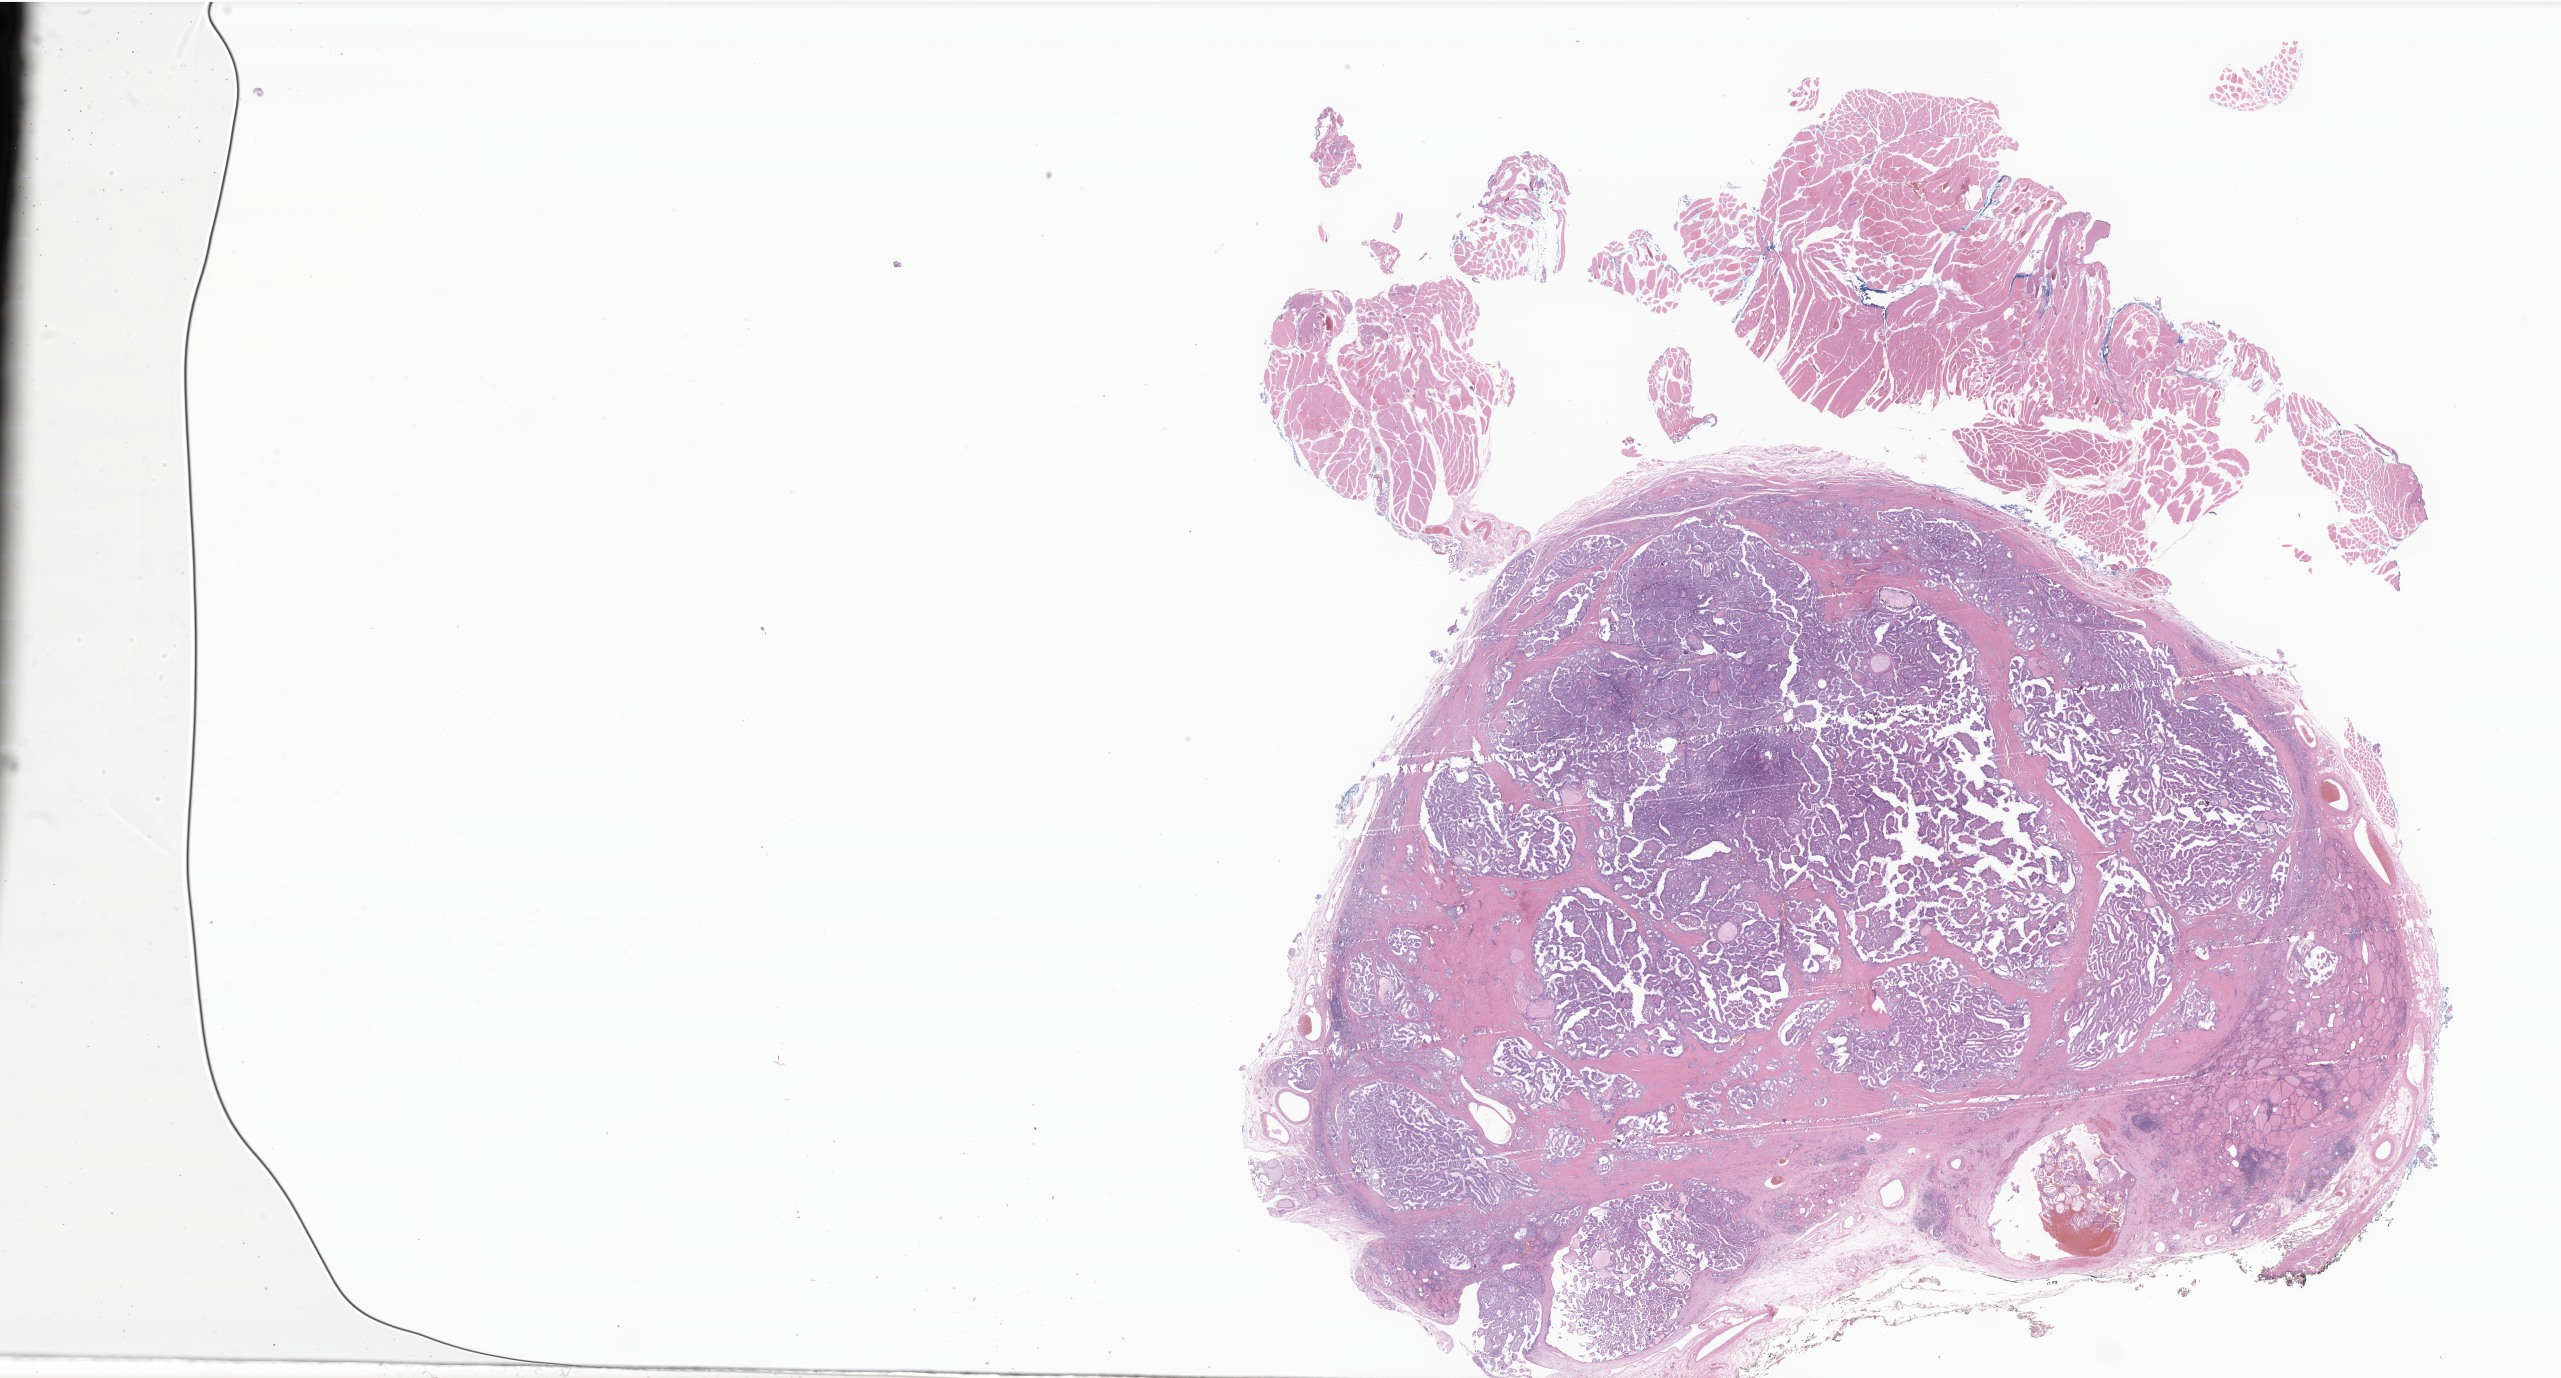
Haematoxylin and eosin whole-slide image of tumor tissue from the thyroid, shown as a low-resolution overview of the whole scanned area (about 43.2 x 23.2 mm), formalin-fixed paraffin-embedded section. Female patient, age 222 months (18 years 6 months).
Recorded diagnosis: Papillary carcinoma, NOS.